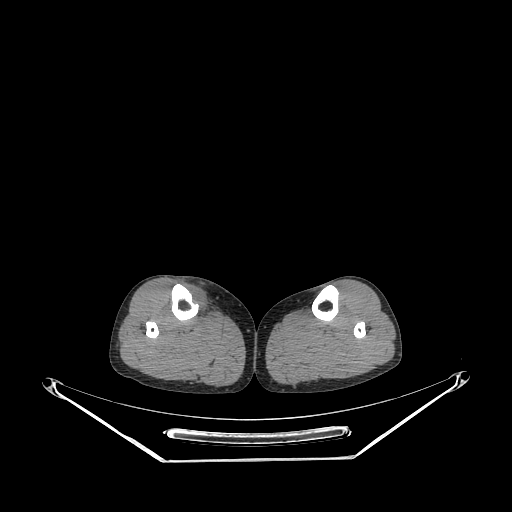
CT of an extremity soft-tissue mass (from a PET/CT study), one axial slice; position 136 of 267 along the scan axis; soft-tissue window (W 400 / L 40 HU); 3.75 mm slice thickness; 512 × 512 image matrix. Female patient. From the clinical record (not read from this slice): histological type: undifferentiated – high grade; grade: high; site of the primary tumour: right thigh.
Annotated regions visible in this slice (expert contour drawn on MRI and transferred to this co-registered scan by the dataset authors):
- gross tumour volume (mass): bounding box <185,285,209,314> (left, top, right, bottom; pixels)